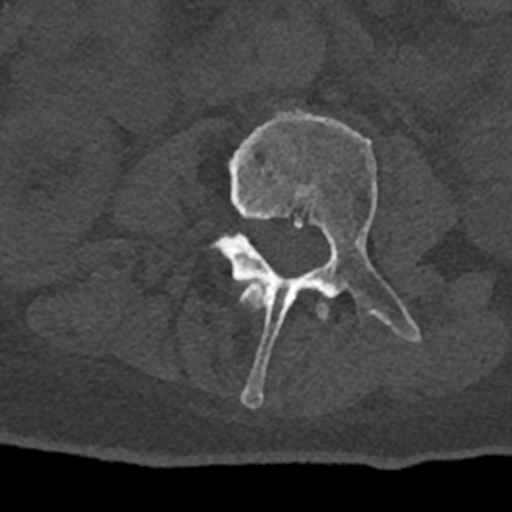
CT including the spine, one axial slice. Position 318 of 797 along the scan axis. 120 kVp. Bone window (W 1800 / L 400 HU). 512 × 512 image matrix, field of view 160 × 160 mm. Patient: male, 74 years. From the clinical record (not read from this slice): primary cancer: renal.
Structures marked on this image (semi-automatic segmentation, software-assisted and operator-edited):
- L2 vertebra: bounding box [x1, y1, x2, y2] px = [240, 282, 328, 319]
- L3 vertebra: [210, 109, 421, 408]